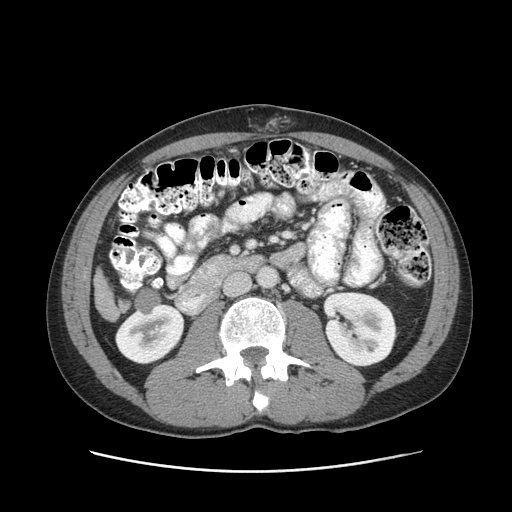
Contrast-enhanced abdominal CT (liver protocol), one axial slice. Position 25 of 93 along the scan axis. Reconstruction kernel STANDARD. 120 kVp. Soft-tissue window (W 400 / L 40 HU). 2.5 mm slice thickness. 512 × 512 image matrix. From the clinical record (not read from this slice): diagnosis: hepatocellular carcinoma (patient treated with transarterial chemoembolisation; whether this scan precedes or follows treatment is not stated here); TNM stage (as recorded): Stage-II; Child-Pugh class: A; tumour differentiation: moderately differentiated; tumour nodularity: multinodular.
Annotated regions visible in this slice (semi-automatic segmentation, software-assisted and operator-edited):
- liver parenchyma outside the tumour (the mass and vessels are separate outlines, so this box may not span the whole liver): box from (x=94, y=269) to (x=114, y=318) px